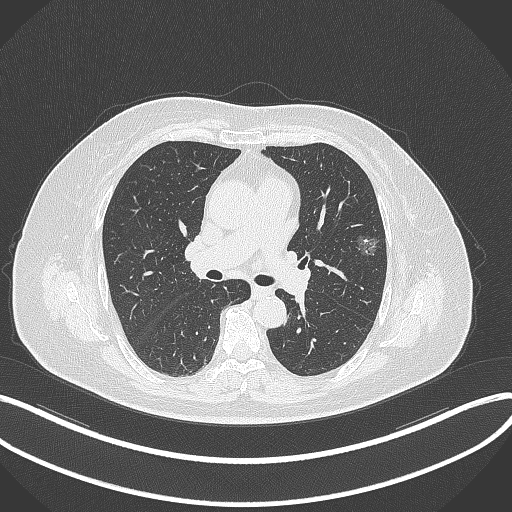
Chest CT, one axial slice. Position 211 of 315 along the scan axis. Reconstruction kernel B70f. 120 kVp. Lung window (W 1500 / L -600 HU). 512 × 512 image matrix. Female patient, age 76 years. Case-level facts recorded for this patient, not image findings: clinical TNM (as recorded): T1b N0 M0; histopathological grade: G1-2.
Outlined on this slice (rectangle marked by the reading radiologist):
- lung tumour (recorded histology: adenocarcinoma): bounding box [x1, y1, x2, y2] px = [354, 231, 383, 258]